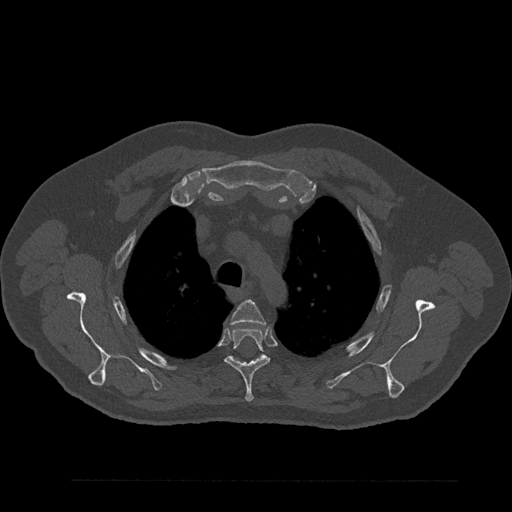
CT including the spine, one axial slice. Position 648 of 797 along the scan axis. Reconstruction kernel Br40s/3. 120 kVp. Bone window (W 1800 / L 400 HU). 512 × 512 image matrix, field of view 430 × 430 mm. Patient: male, 61 years. From the clinical record (not read from this slice): primary cancer: prostate.
Annotated regions visible in this slice (semi-automatic segmentation, software-assisted and operator-edited):
- T3 vertebra: bounding box <231,300,266,325> (left, top, right, bottom; pixels)
- T4 vertebra: <225,327,270,402>
- T5 vertebra: <235,356,264,360>